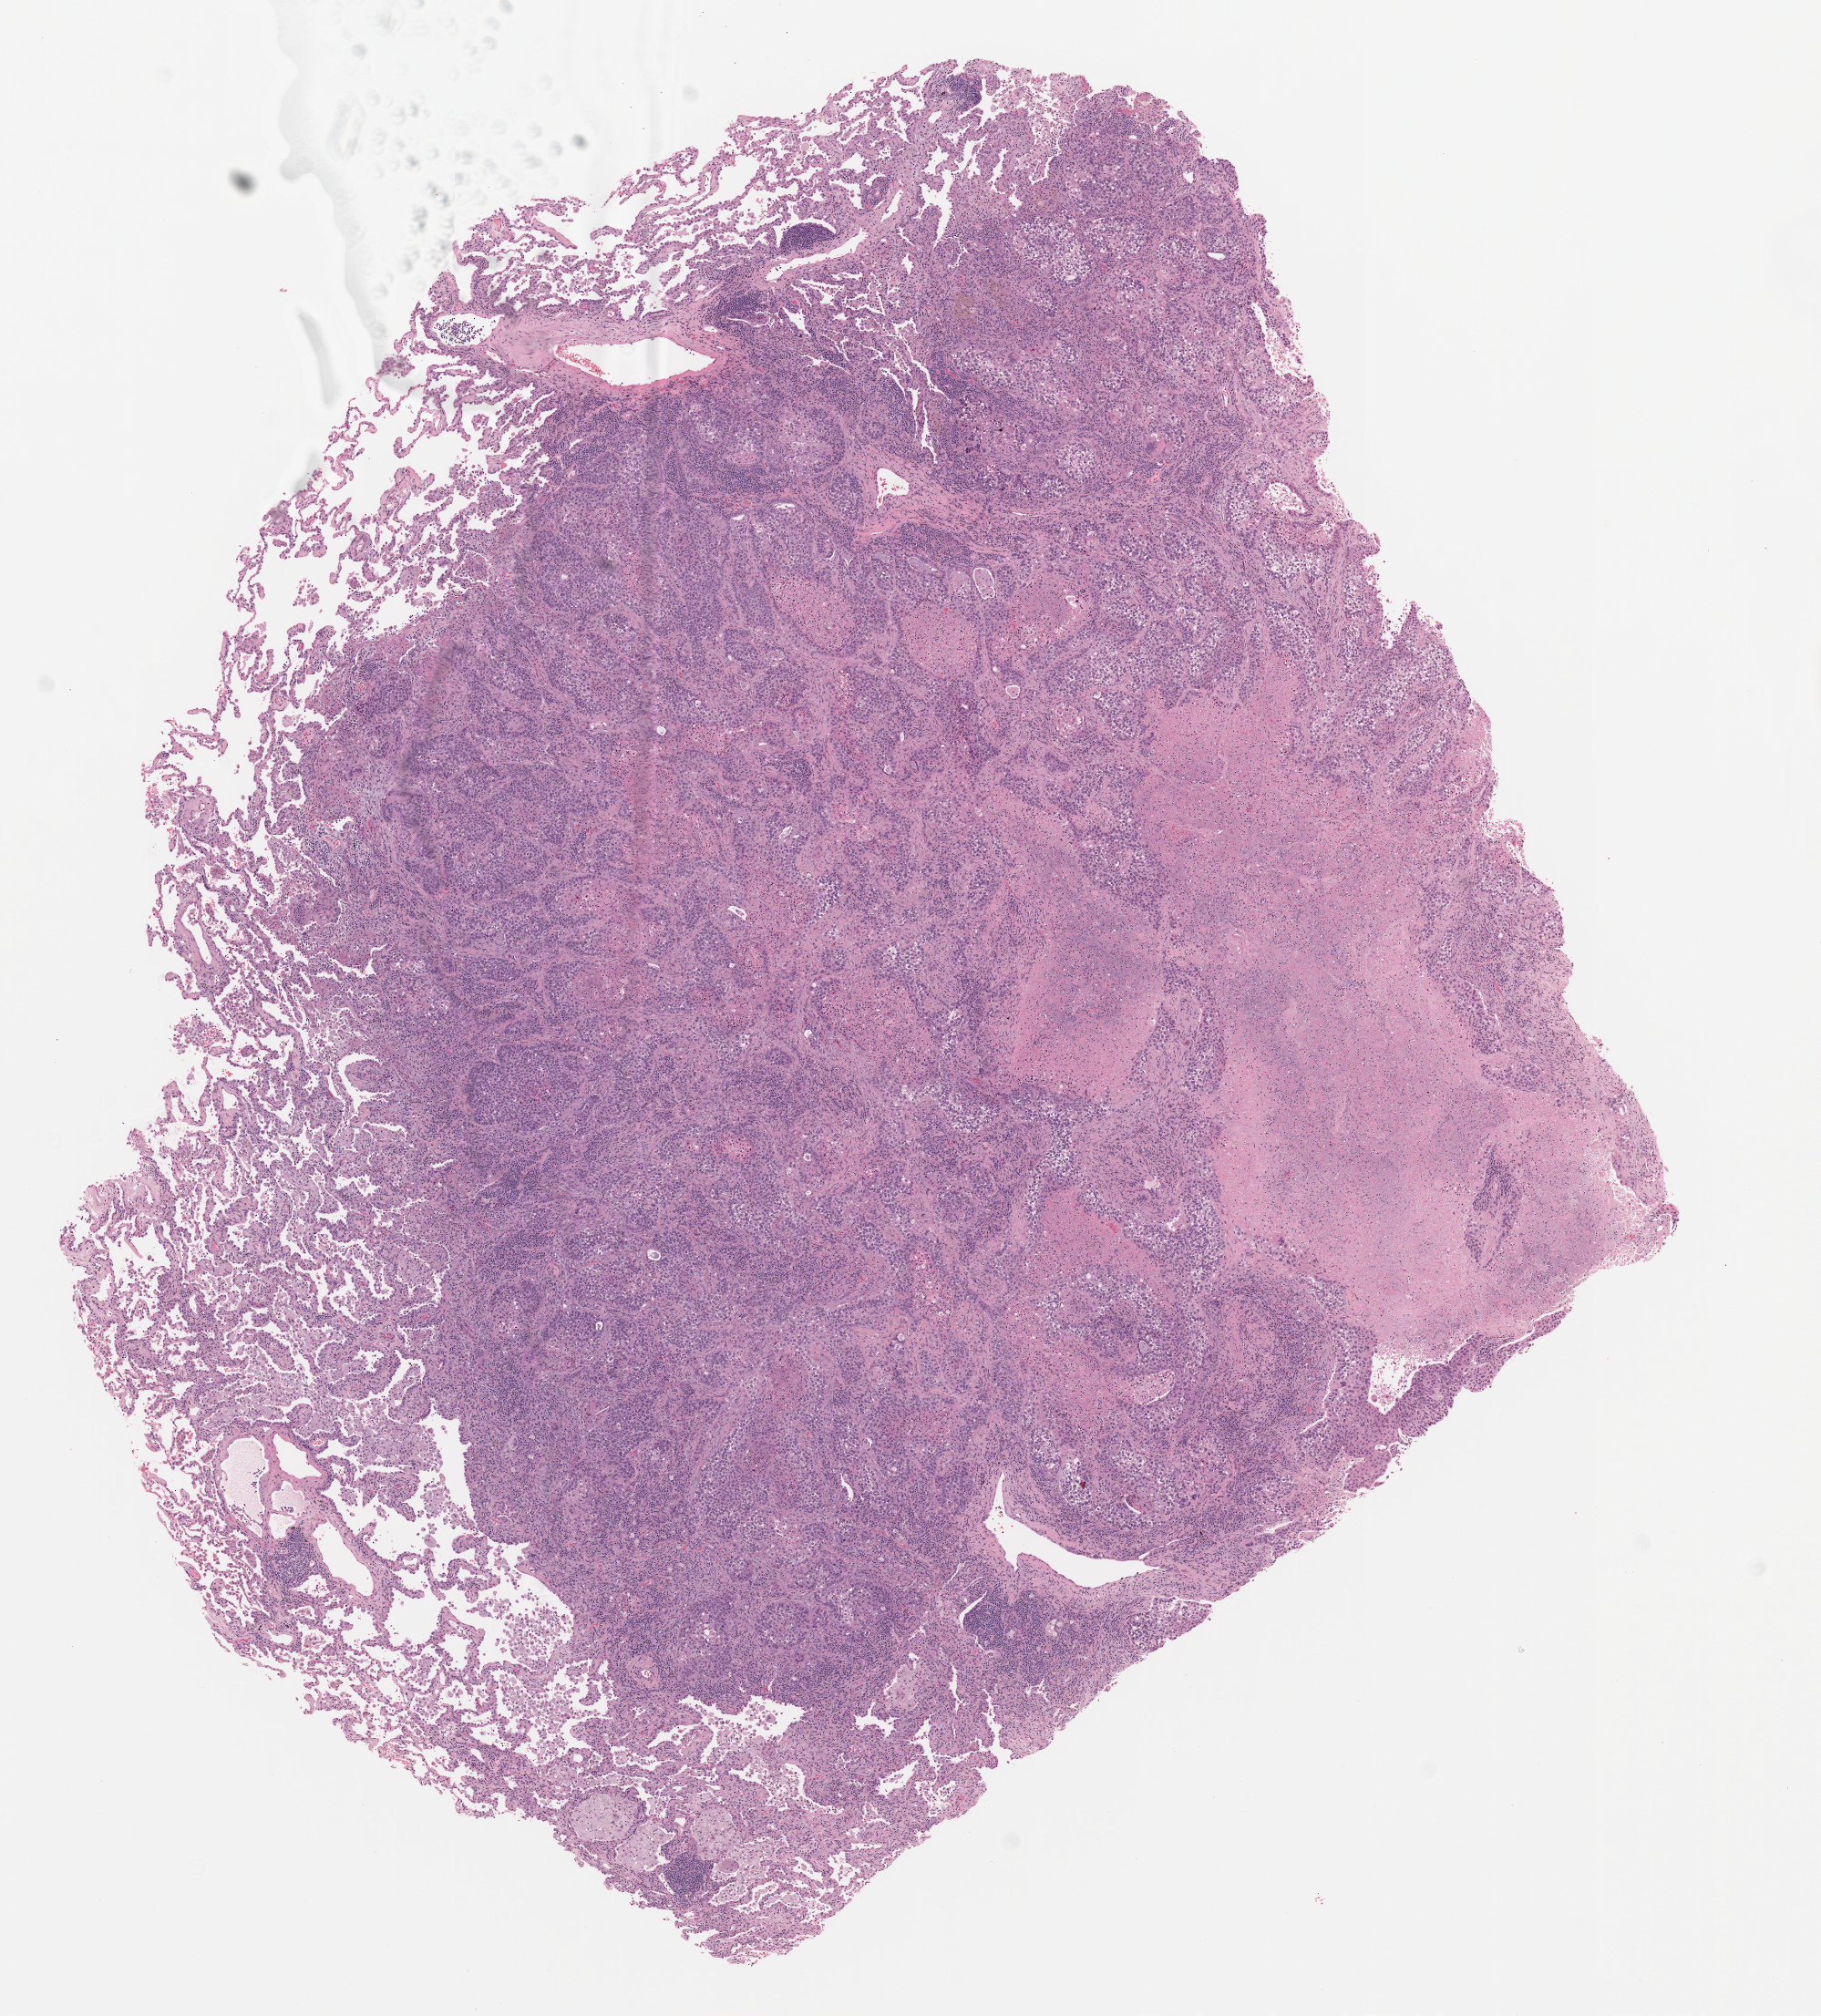
Digitized H&E tissue section (whole slide), a low-resolution overview of the entire scanned area, about 8.0 x 8.9 mm (acquisition: 20x scan), formalin-fixed paraffin-embedded (FFPE) diagnostic section, sample: primary tumour, lung. Female patient.
* TNM: T1 N0 M0
* histologic diagnosis: Squamous cell carcinoma, NOS (upper lobe, lung)
* laterality: left
* AJCC pathologic stage: IA (6th edition)